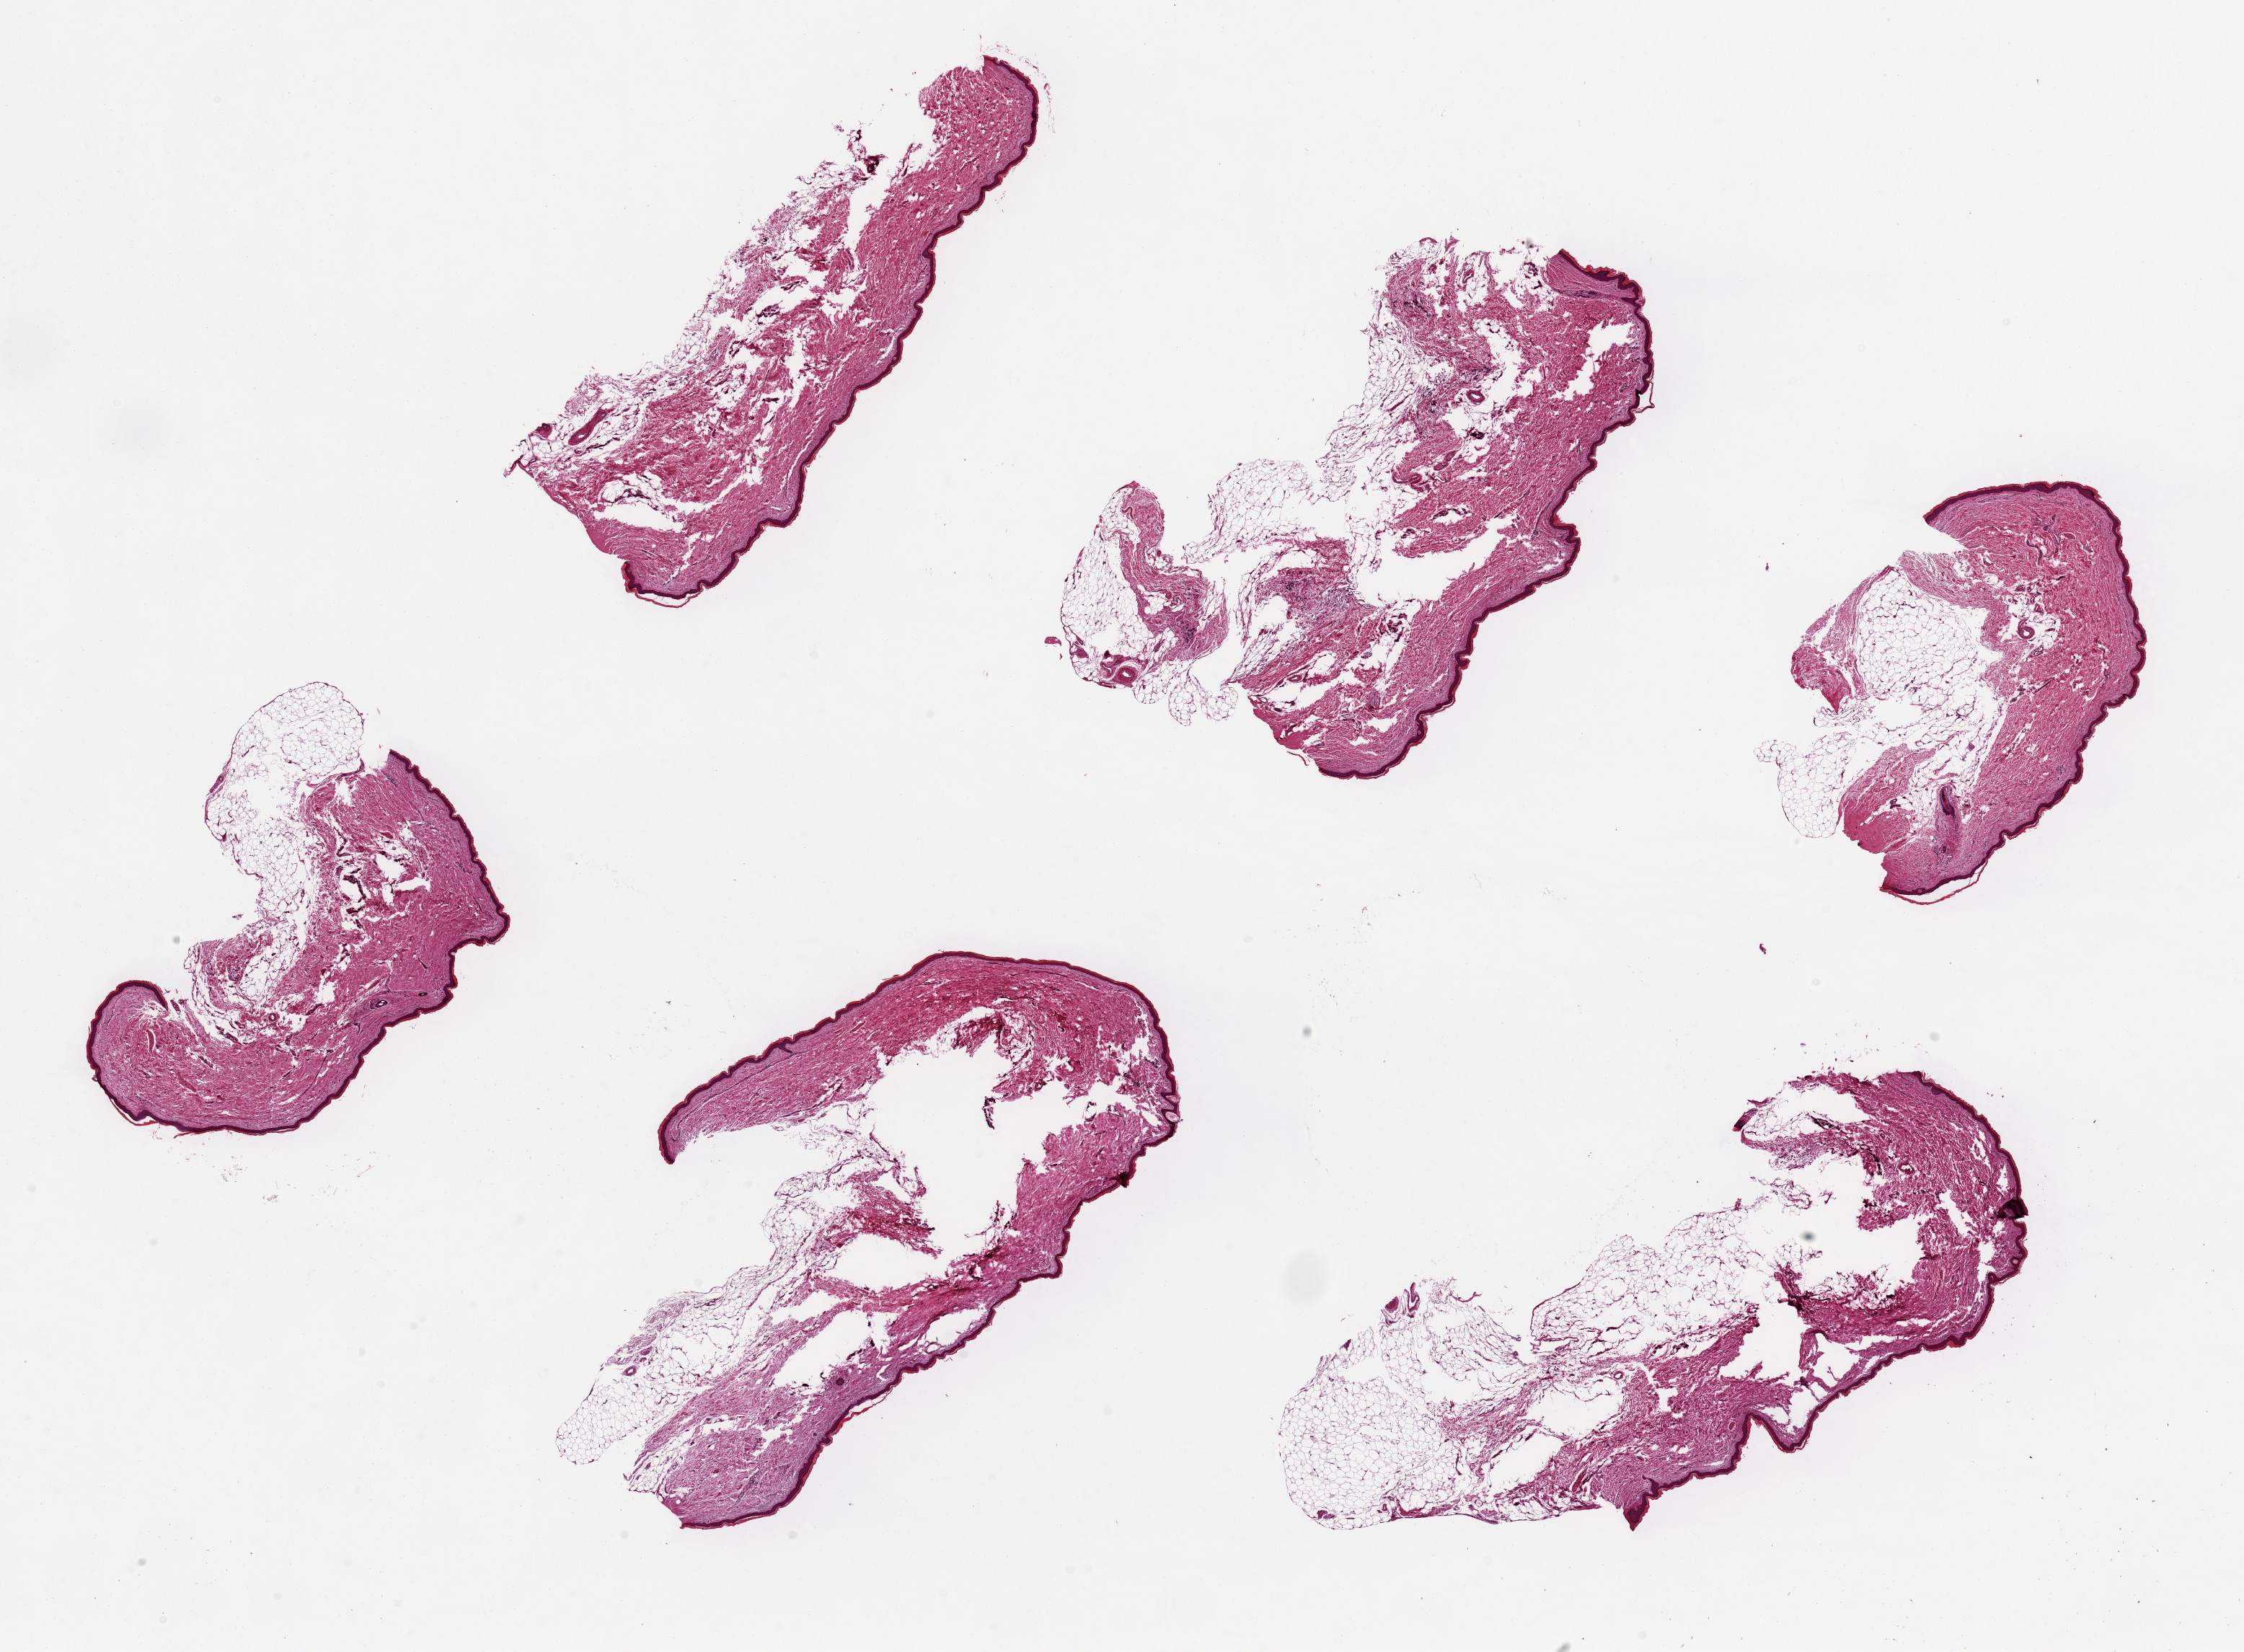
Hematoxylin and eosin (H&E) whole-slide image, brightfield — low-resolution overview of the scanned area, about 24.6 x 18.1 mm, PAXgene-fixed, paraffin-embedded tissue, section of skin of lower leg (target tissue), donor tissue sample. Female donor.
Reviewer comment on this tissue sample: 6 pieces up to 7x3.8 mm; 5 pieces have up to 1.5 mm subcutaneous adipose.